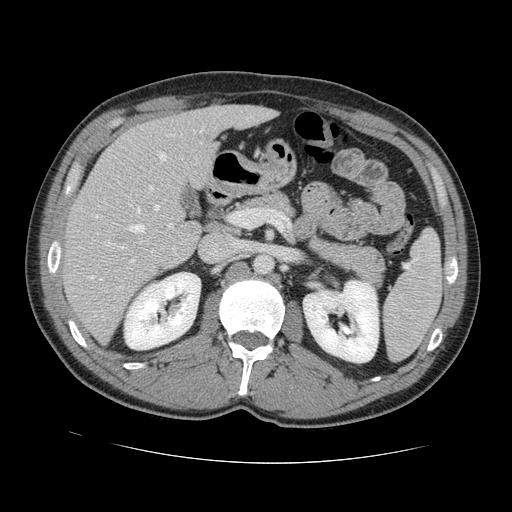
Contrast-enhanced abdominal CT, one axial slice. Position 73 of 131 along the scan axis. Intravenous contrast given. Soft-tissue window (W 400 / L 40 HU). 512 × 512 image matrix, field of view 380 × 380 mm. Male patient, age 40 years. Case-level facts recorded for this patient, not image findings: diagnosis: colorectal cancer liver metastases, imaged before liver resection.
Outlined on this slice (manually delineated by an expert):
- hepatic veins: bounding box [x1, y1, x2, y2] px = [90, 152, 167, 280]
- liver: [66, 106, 272, 342]
- planned liver remnant (the part of the liver to remain after resection): [107, 106, 272, 193]
- portal vein (with intrahepatic branches): [130, 185, 233, 263]